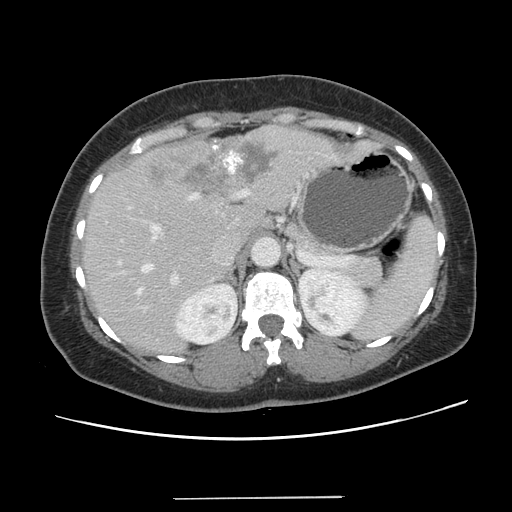
Contrast-enhanced abdominal CT, one axial slice; slice 89 of 141 in the series (ordered by position); intravenous contrast given; soft-tissue window (W 400 / L 40 HU); 512 × 512 image matrix, field of view 366 × 366 mm. Female patient, age 53 years. Case-level facts recorded for this patient, not image findings: diagnosis: colorectal cancer liver metastases, imaged before liver resection; multiple liver metastases: no; largest metastasis: 14.5 cm; disease in both lobes: yes.
Outlined on this slice (expert manual segmentation):
- hepatic veins: bounding box <137,195,195,294> (left, top, right, bottom; pixels)
- liver: <84,127,373,353>
- planned liver remnant (the part of the liver to remain after resection): <84,208,263,353>
- portal vein (with intrahepatic branches): <151,190,246,287>
- liver metastasis: <145,141,277,195>